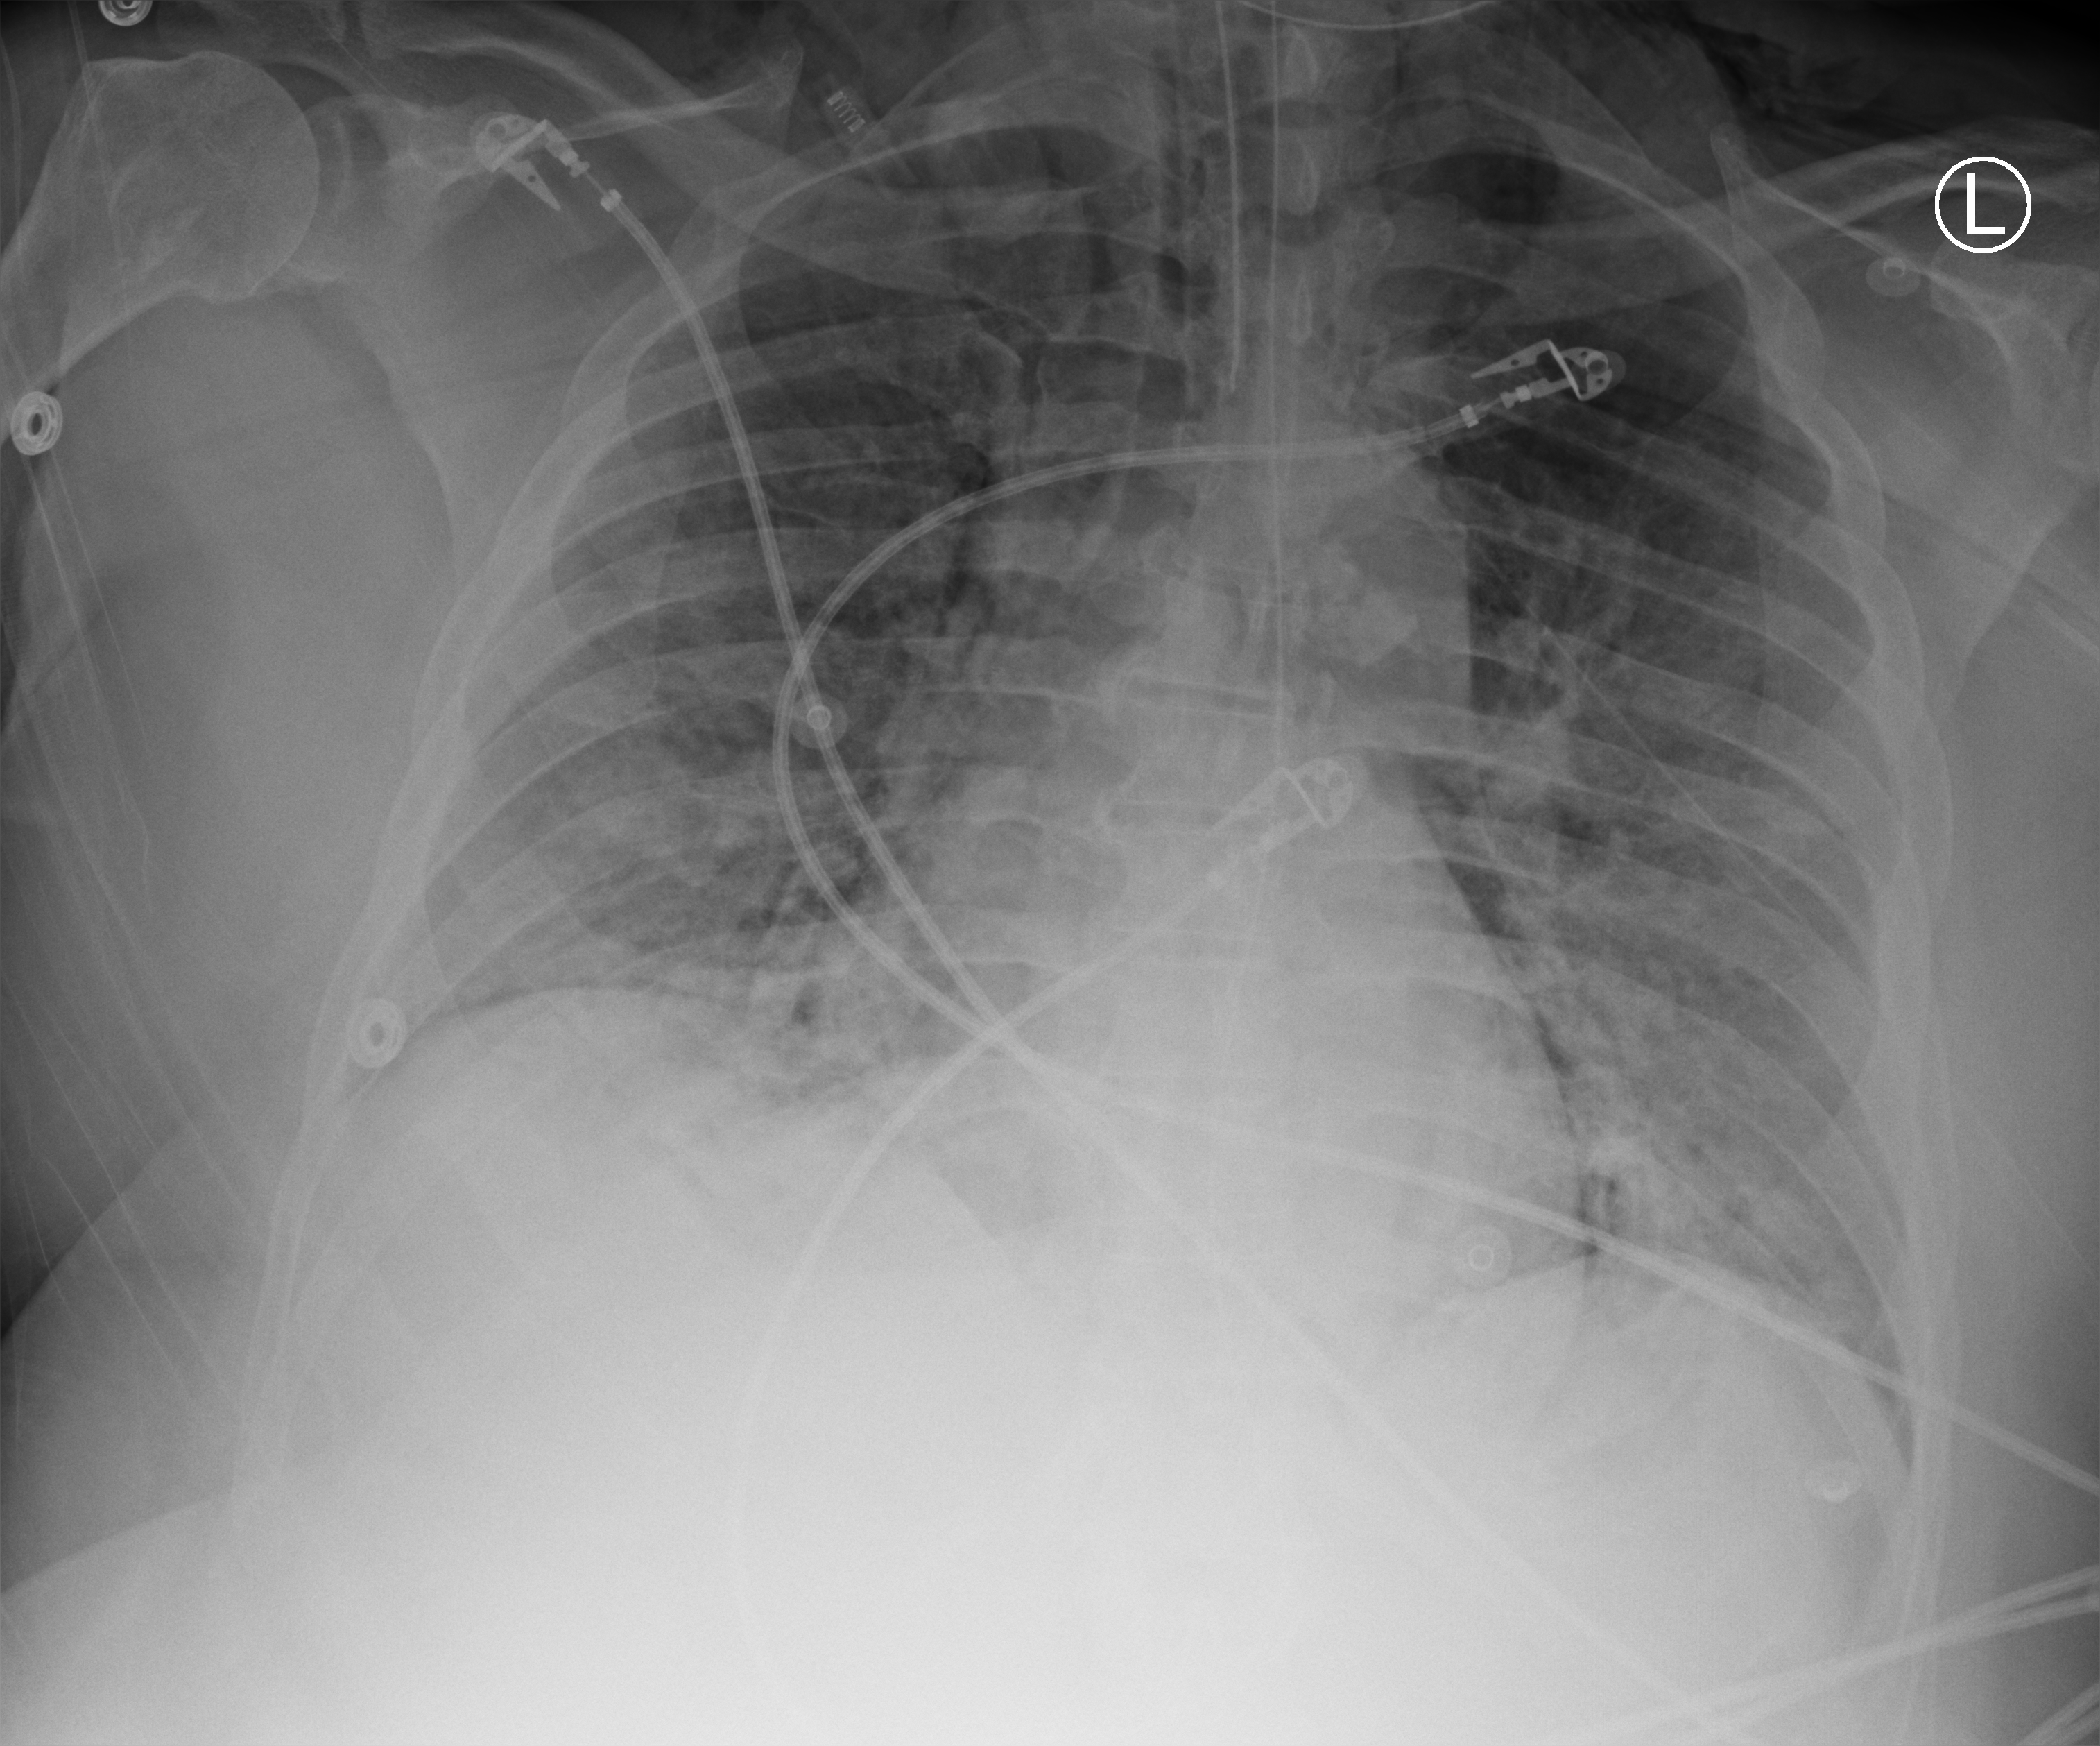
Chest X-ray (portable), anteroposterior (AP) projection. Male patient hospitalised with COVID-19, age 18–59 years.
Hospital-stay facts (about this admission, not read from this image; timing relative to this image not recorded):
- chronic kidney disease (admission record): no